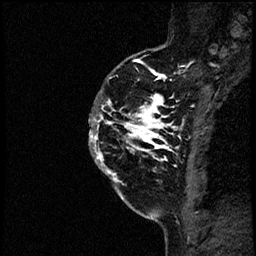
Breast MRI (dynamic contrast-enhanced), one sagittal slice; position 45 of 60 along the scan axis; dynamic contrast-enhanced study with each time point stored as its own series, time point 2 of 4 at this slice position (early post-contrast, ordered by acquisition time); 1.5 T; TE 4.2 ms, TR 17.6 ms; 2 mm slice thickness; 256 × 256 image matrix, field of view 200 × 200 mm. Patient: female, 40 years. From the clinical record (not read from this slice): setting: breast cancer imaged before/during neoadjuvant chemotherapy; receptor status: HER2-positive.
Structures marked on this image (semi-automatic segmentation, software-assisted and operator-edited):
- analysis volume of interest (the breast-tissue region the enhancement analysis was run in; not a lesion): box from (x=90, y=56) to (x=197, y=205) px
- tumour enhancement mask (voxels above the 100 % enhancement threshold inside the analysis volume of interest): (x=91, y=60)–(x=188, y=186)